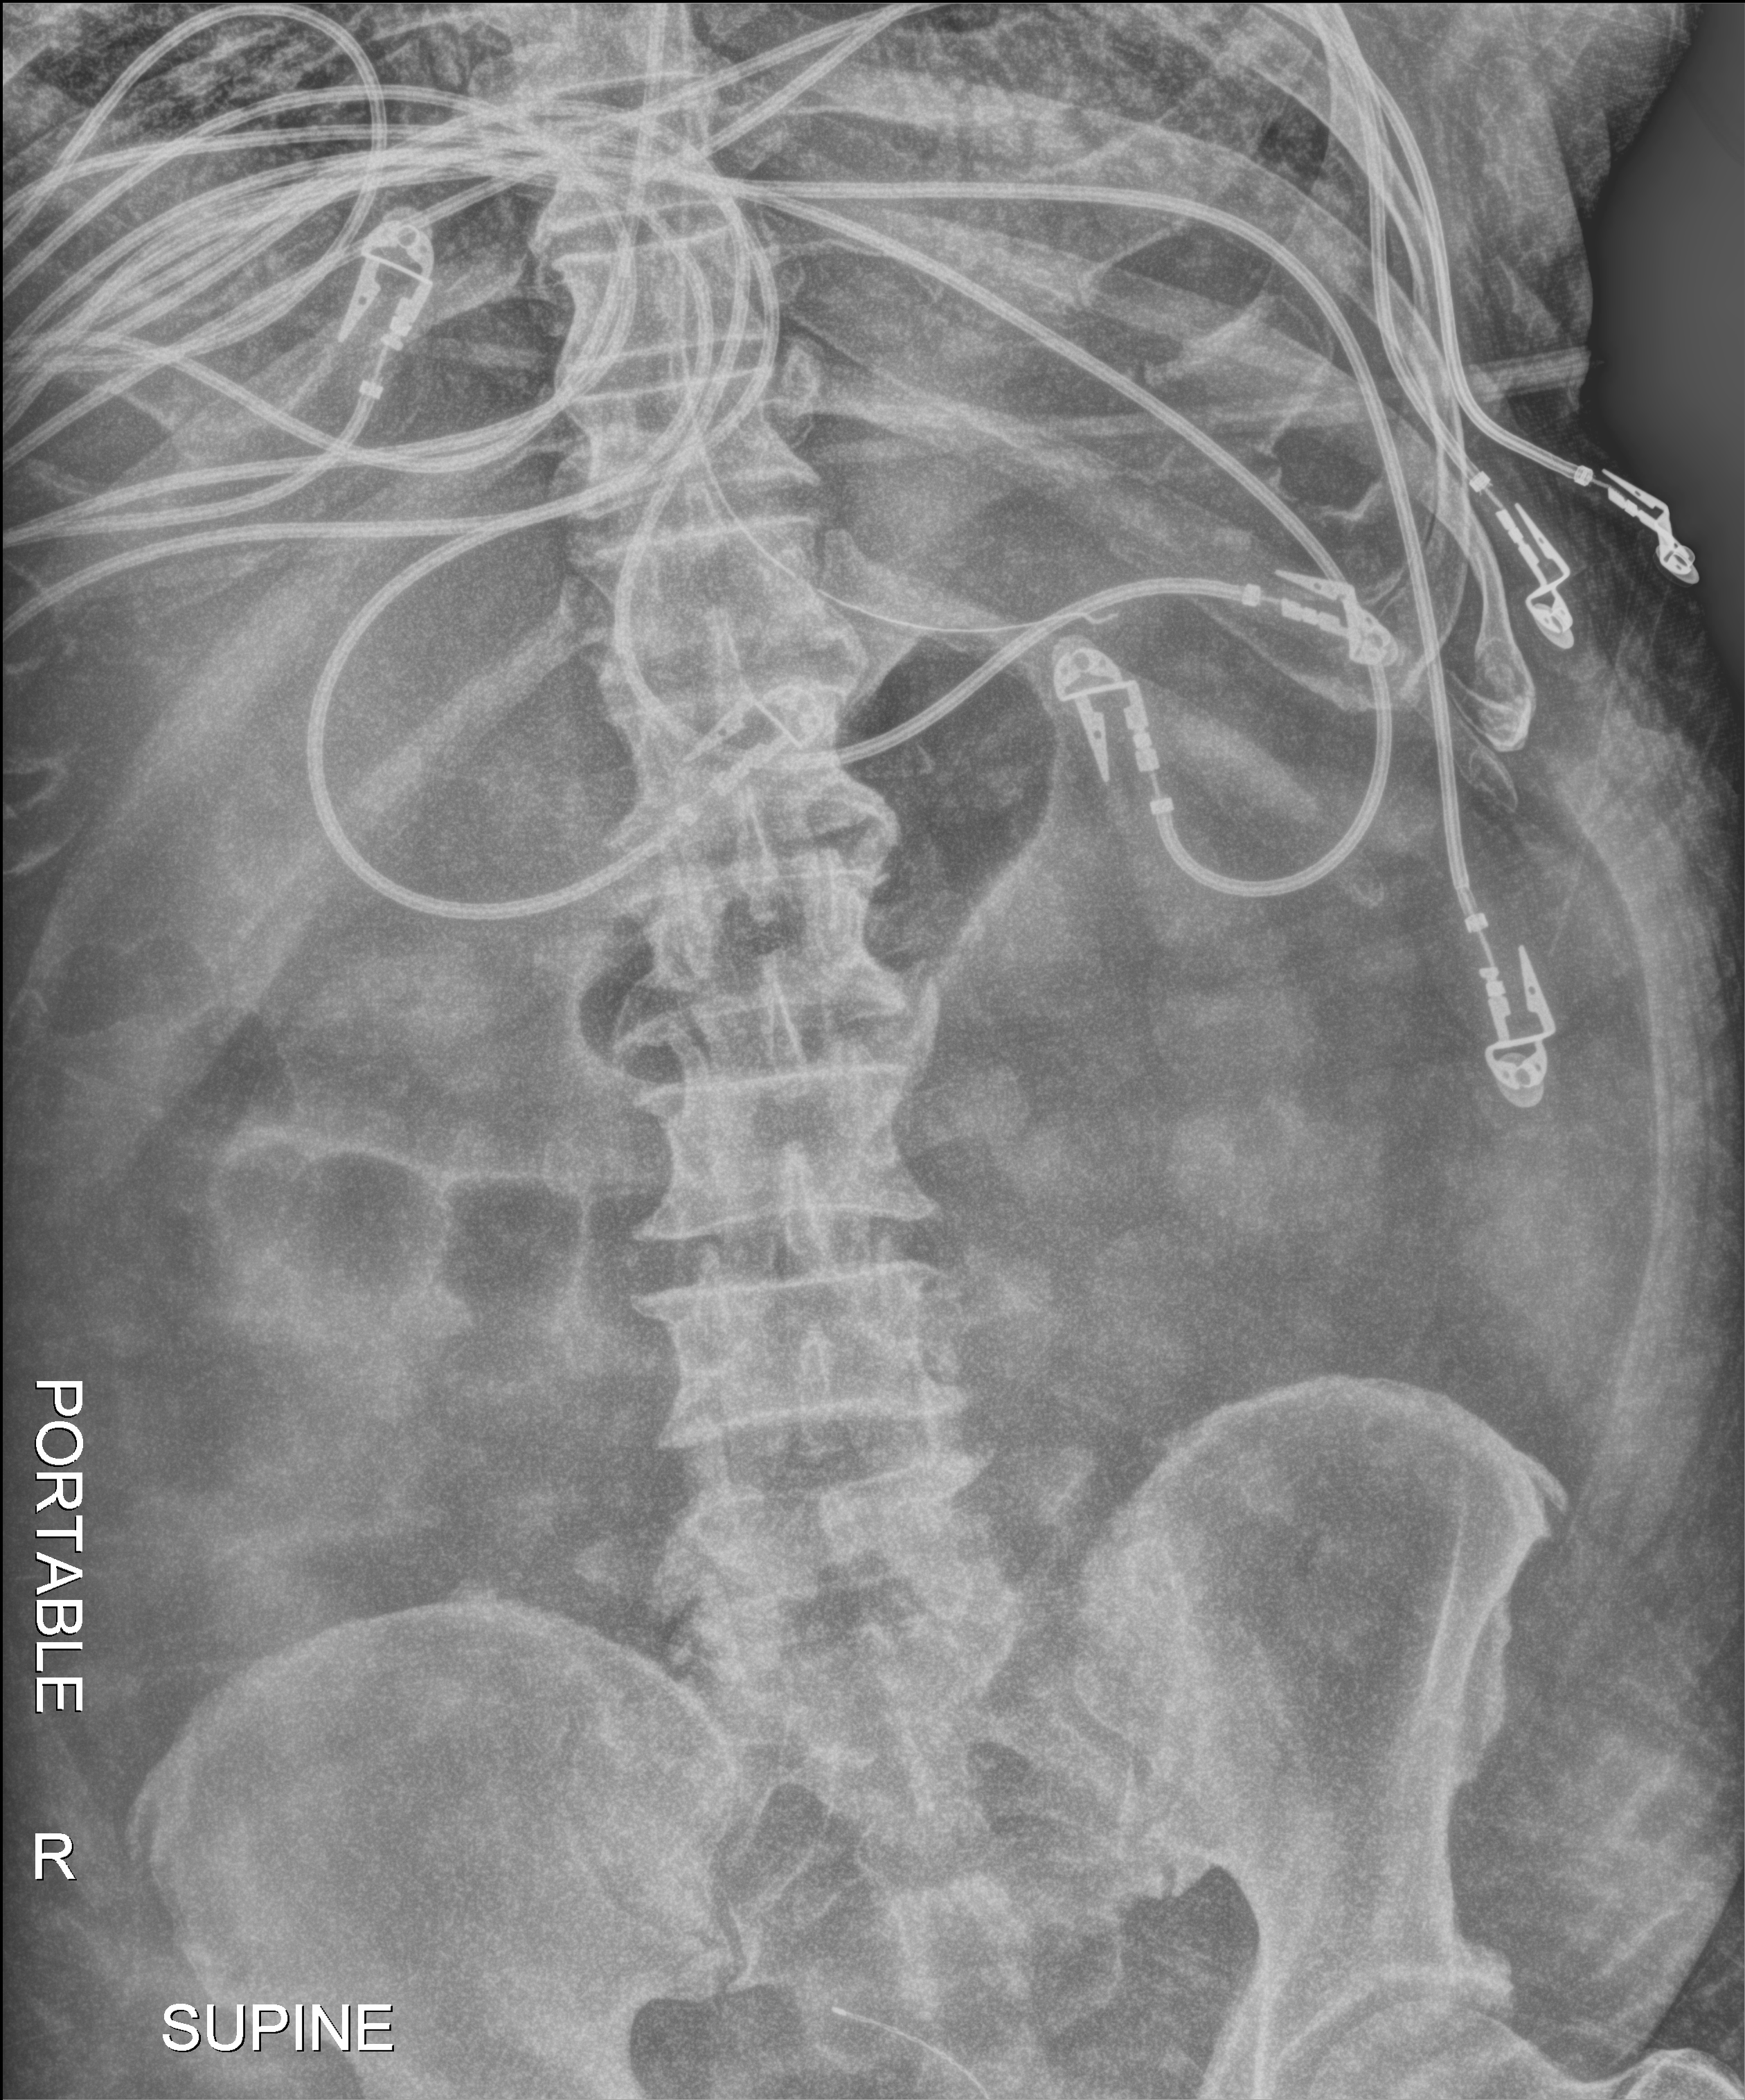
Portable abdomen radiograph; anteroposterior (AP) projection. Male patient hospitalised with COVID-19, age 75–90 years.
Admission-level facts for this patient (not findings on this image; timing relative to this image not recorded): other chronic lung disease (admission record): no; admitted to intensive care during this hospital stay: yes.